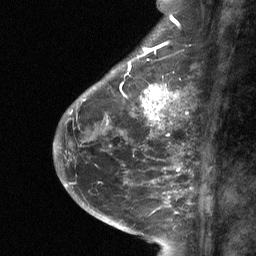
Breast MRI (dynamic contrast-enhanced), one sagittal slice; dynamic contrast-enhanced study with each time point stored as its own series, time point 2 of 3 at this slice position (early post-contrast, ordered by acquisition time); 1.5 T; TE 4.8 ms, TR 27 ms; 256 × 256 image matrix, field of view 180 × 180 mm. Patient: female, 59 years. From the clinical record (not read from this slice): setting: breast cancer imaged before/during neoadjuvant chemotherapy; receptor status: triple-negative.
Structures marked on this image (semi-automatic segmentation, software-assisted and operator-edited):
- analysis volume of interest (the breast-tissue region the enhancement analysis was run in; not a lesion): box from (x=113, y=80) to (x=175, y=120) px
- tumour enhancement mask (voxels above the 90 % enhancement threshold inside the analysis volume of interest): (x=142, y=87)–(x=175, y=120)